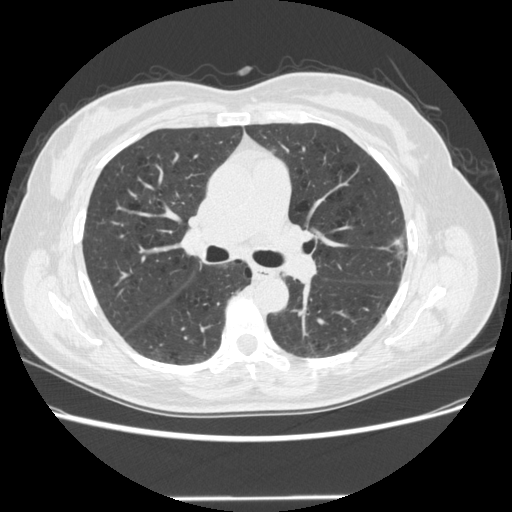
Axial slice from a low-dose chest CT screening exam; baseline annual screen; lung window (W 1500 / L -600 HU); 120 kVp. Female participant, aged 61 years at enrolment. Current smoker at enrolment.
Expert reader's lesion annotation, box from (x=383, y=227) to (x=427, y=278) px. Screening reader's record for this exam: no non-calcified nodule ≥4 mm recorded. Official screen result: negative screen, minor abnormalities not suspicious for lung cancer. Lung cancer was diagnosed 791 days after this screen: bronchiolo-alveolar adenocarcinoma, NOS, left upper lobe, well differentiated (G1), stage IA (AJCC 6th edition), 11 mm at pathology.